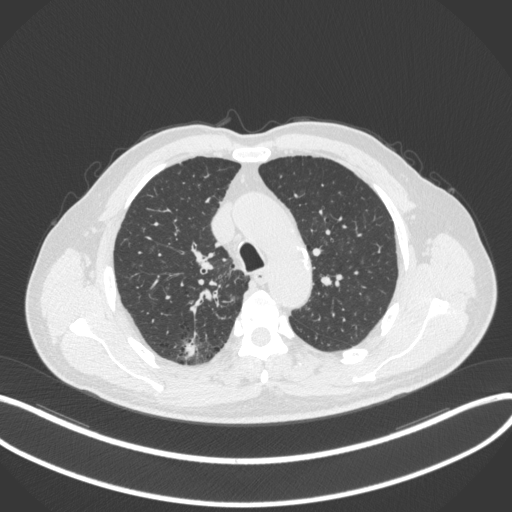
Chest CT, one axial slice. Slice 273 of 366 in the series (ordered by position). Reconstruction kernel B31f. 120 kVp. Lung window (W 1500 / L -600 HU). 1 mm slice thickness. 512 × 512 image matrix, field of view 400 × 400 mm. Patient: male, 69 years. From the clinical record (not read from this slice): clinical TNM (as recorded): T1b N0 M0; histopathological grade: G2-3.
Structures marked on this image (bounding box drawn by a radiologist):
- lung tumour (recorded histology: adenocarcinoma): bounding box [x1, y1, x2, y2] px = [180, 337, 196, 361]